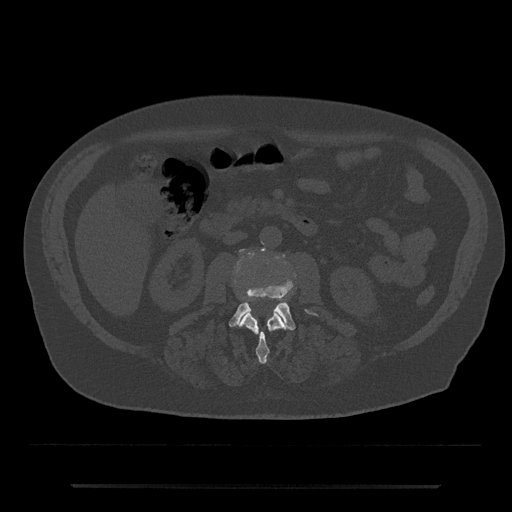
CT including the spine, one axial slice; 120 kVp; bone window (W 1800 / L 400 HU); 0.5 mm slice thickness; 512 × 512 image matrix, field of view 434 × 434 mm. Male patient, age 80 years. Case-level facts recorded for this patient, not image findings: primary cancer: prostate; vertebrae with lytic lesions (as recorded): L1, T11.
Structures marked on this image (semi-automatic segmentation, software-assisted and operator-edited):
- L2 vertebra: bounding box [x1, y1, x2, y2] px = [239, 310, 287, 364]
- L3 vertebra: [229, 249, 312, 330]